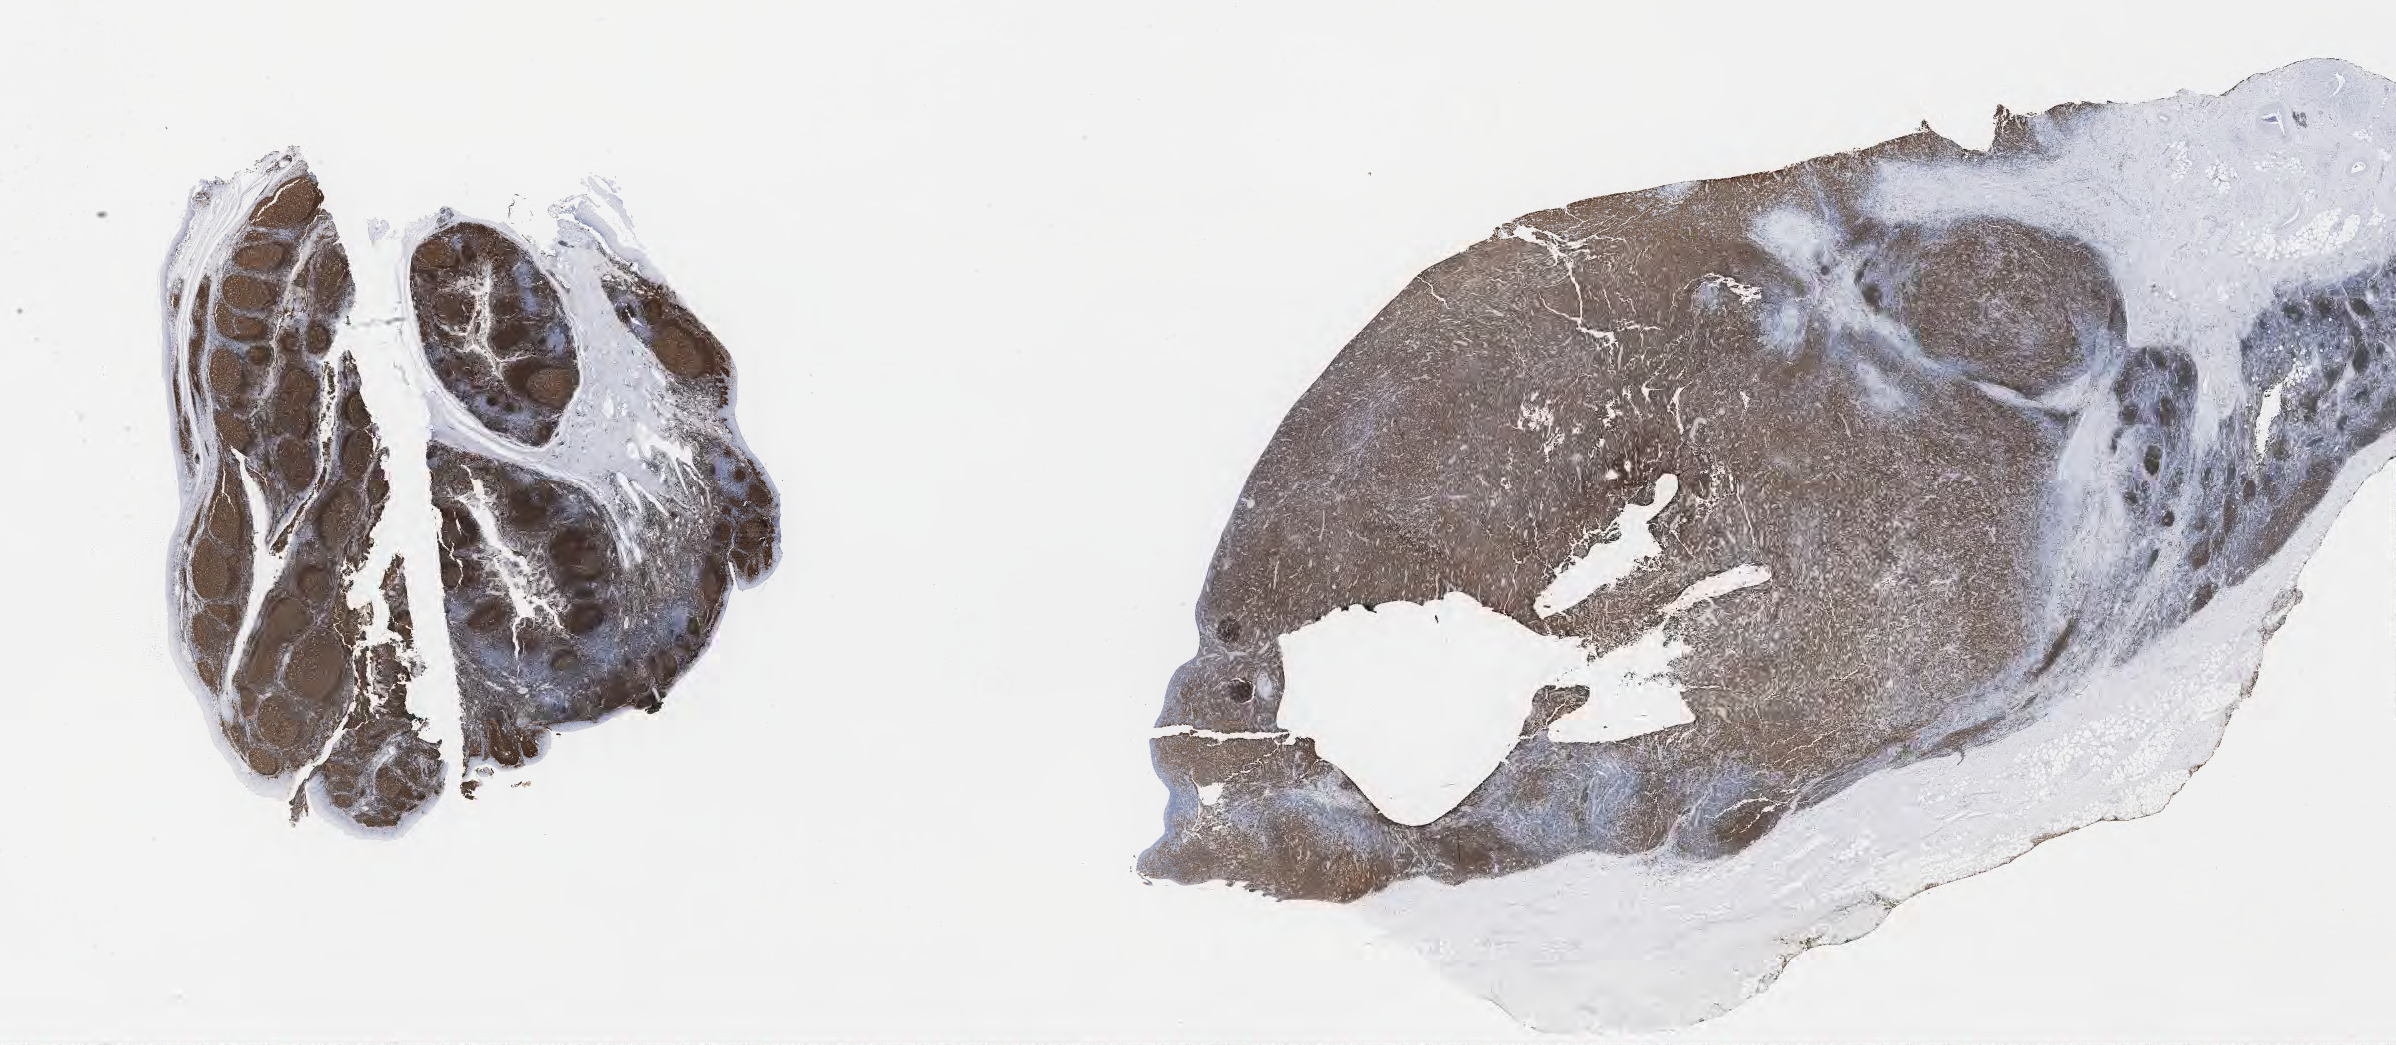
Whole-slide image, immunohistochemical stain for CD79a — shown as a low-resolution overview of the whole scanned area (about 38.7 x 16.9 mm); tumor tissue; site: lymph node. Patient: male, 60 years old.
- diagnosis: Diffuse large B-cell lymphoma, NOS